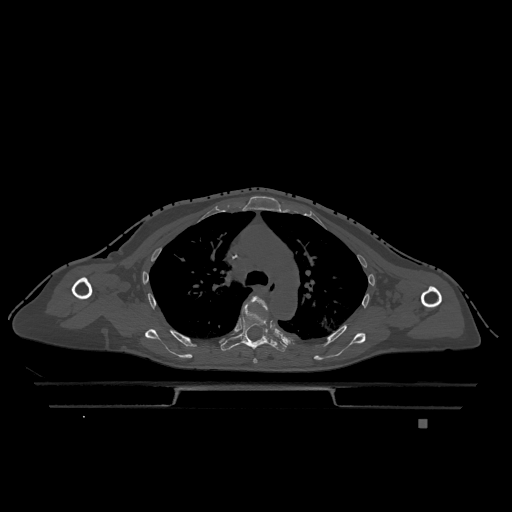
CT including the spine, one axial slice; position 849 of 1317 along the scan axis; bone window (W 1800 / L 400 HU); 0.5 mm slice thickness; 512 × 512 image matrix, field of view 500 × 500 mm. Patient: female, 74 years. From the clinical record (not read from this slice): primary cancer: lung.
Outlined on this slice (semi-automatically segmented with operator editing):
- T4 vertebra: bounding box <249,296,268,364> (left, top, right, bottom; pixels)
- T5 vertebra: <221,303,287,353>